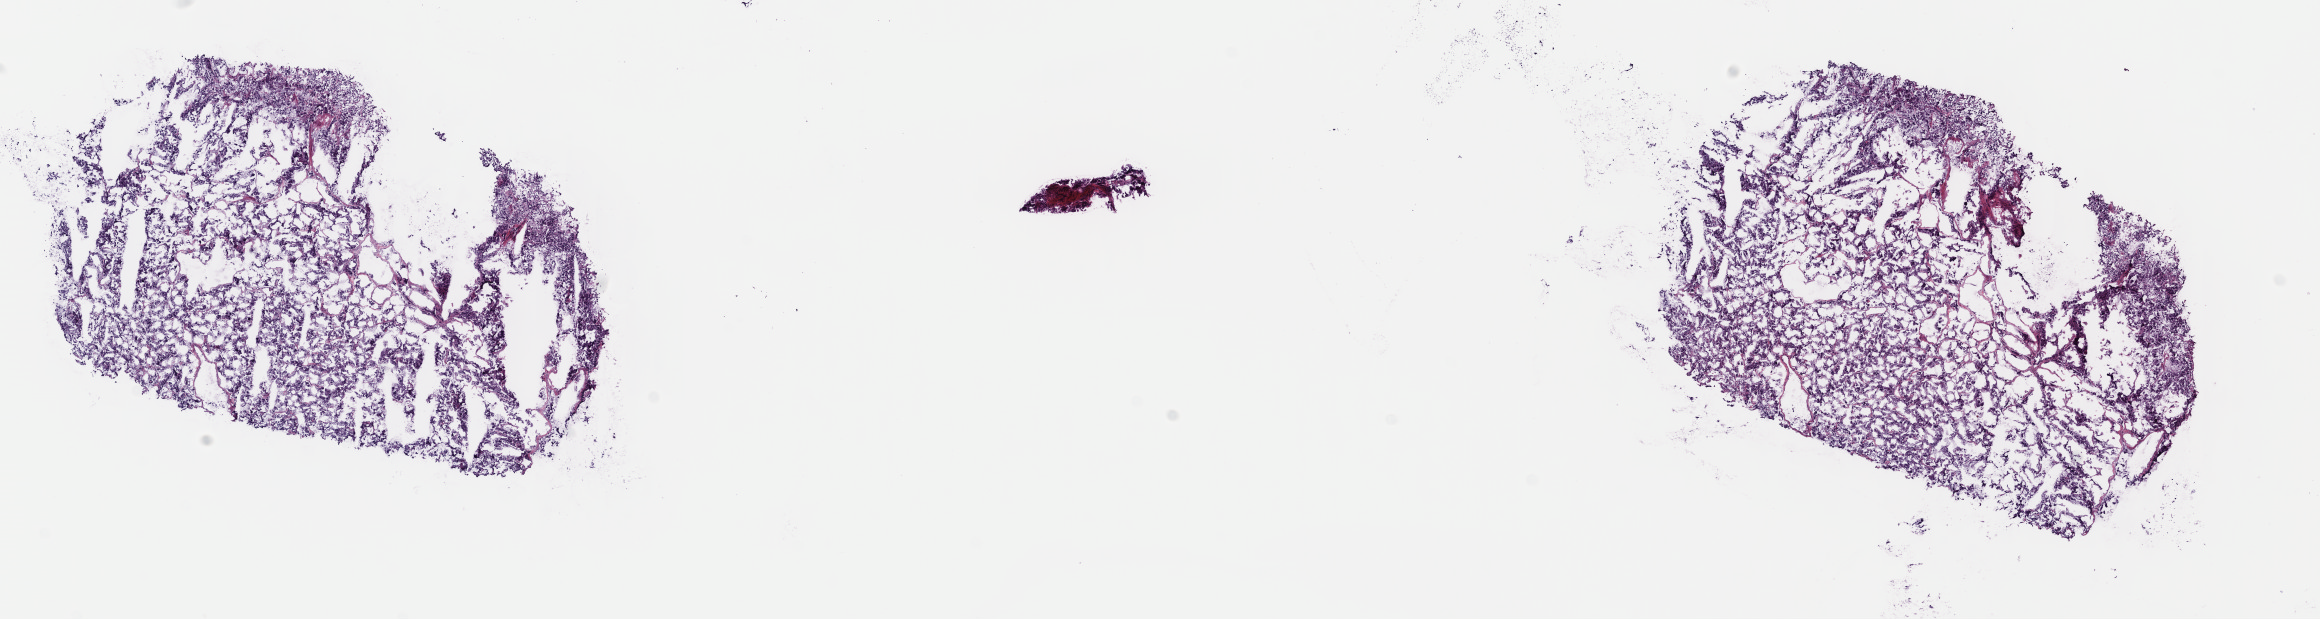
H&E whole-slide image — a low-resolution overview of the entire scanned area, about 18.2 x 4.9 mm; frozen section; sample: primary tumour, adrenal gland. Female, age 64 years at initial diagnosis. Pathologist review of this section (percent, as recorded): tumour cells 80%, tumour nuclei 80%, normal cells 0%, stromal cells 20%, necrosis 0%. Infiltration values recorded for this section: lymphocyte infiltration 0%, monocyte infiltration 0%, neutrophil infiltration 0%.
Diagnosis: Pheochromocytoma, NOS.